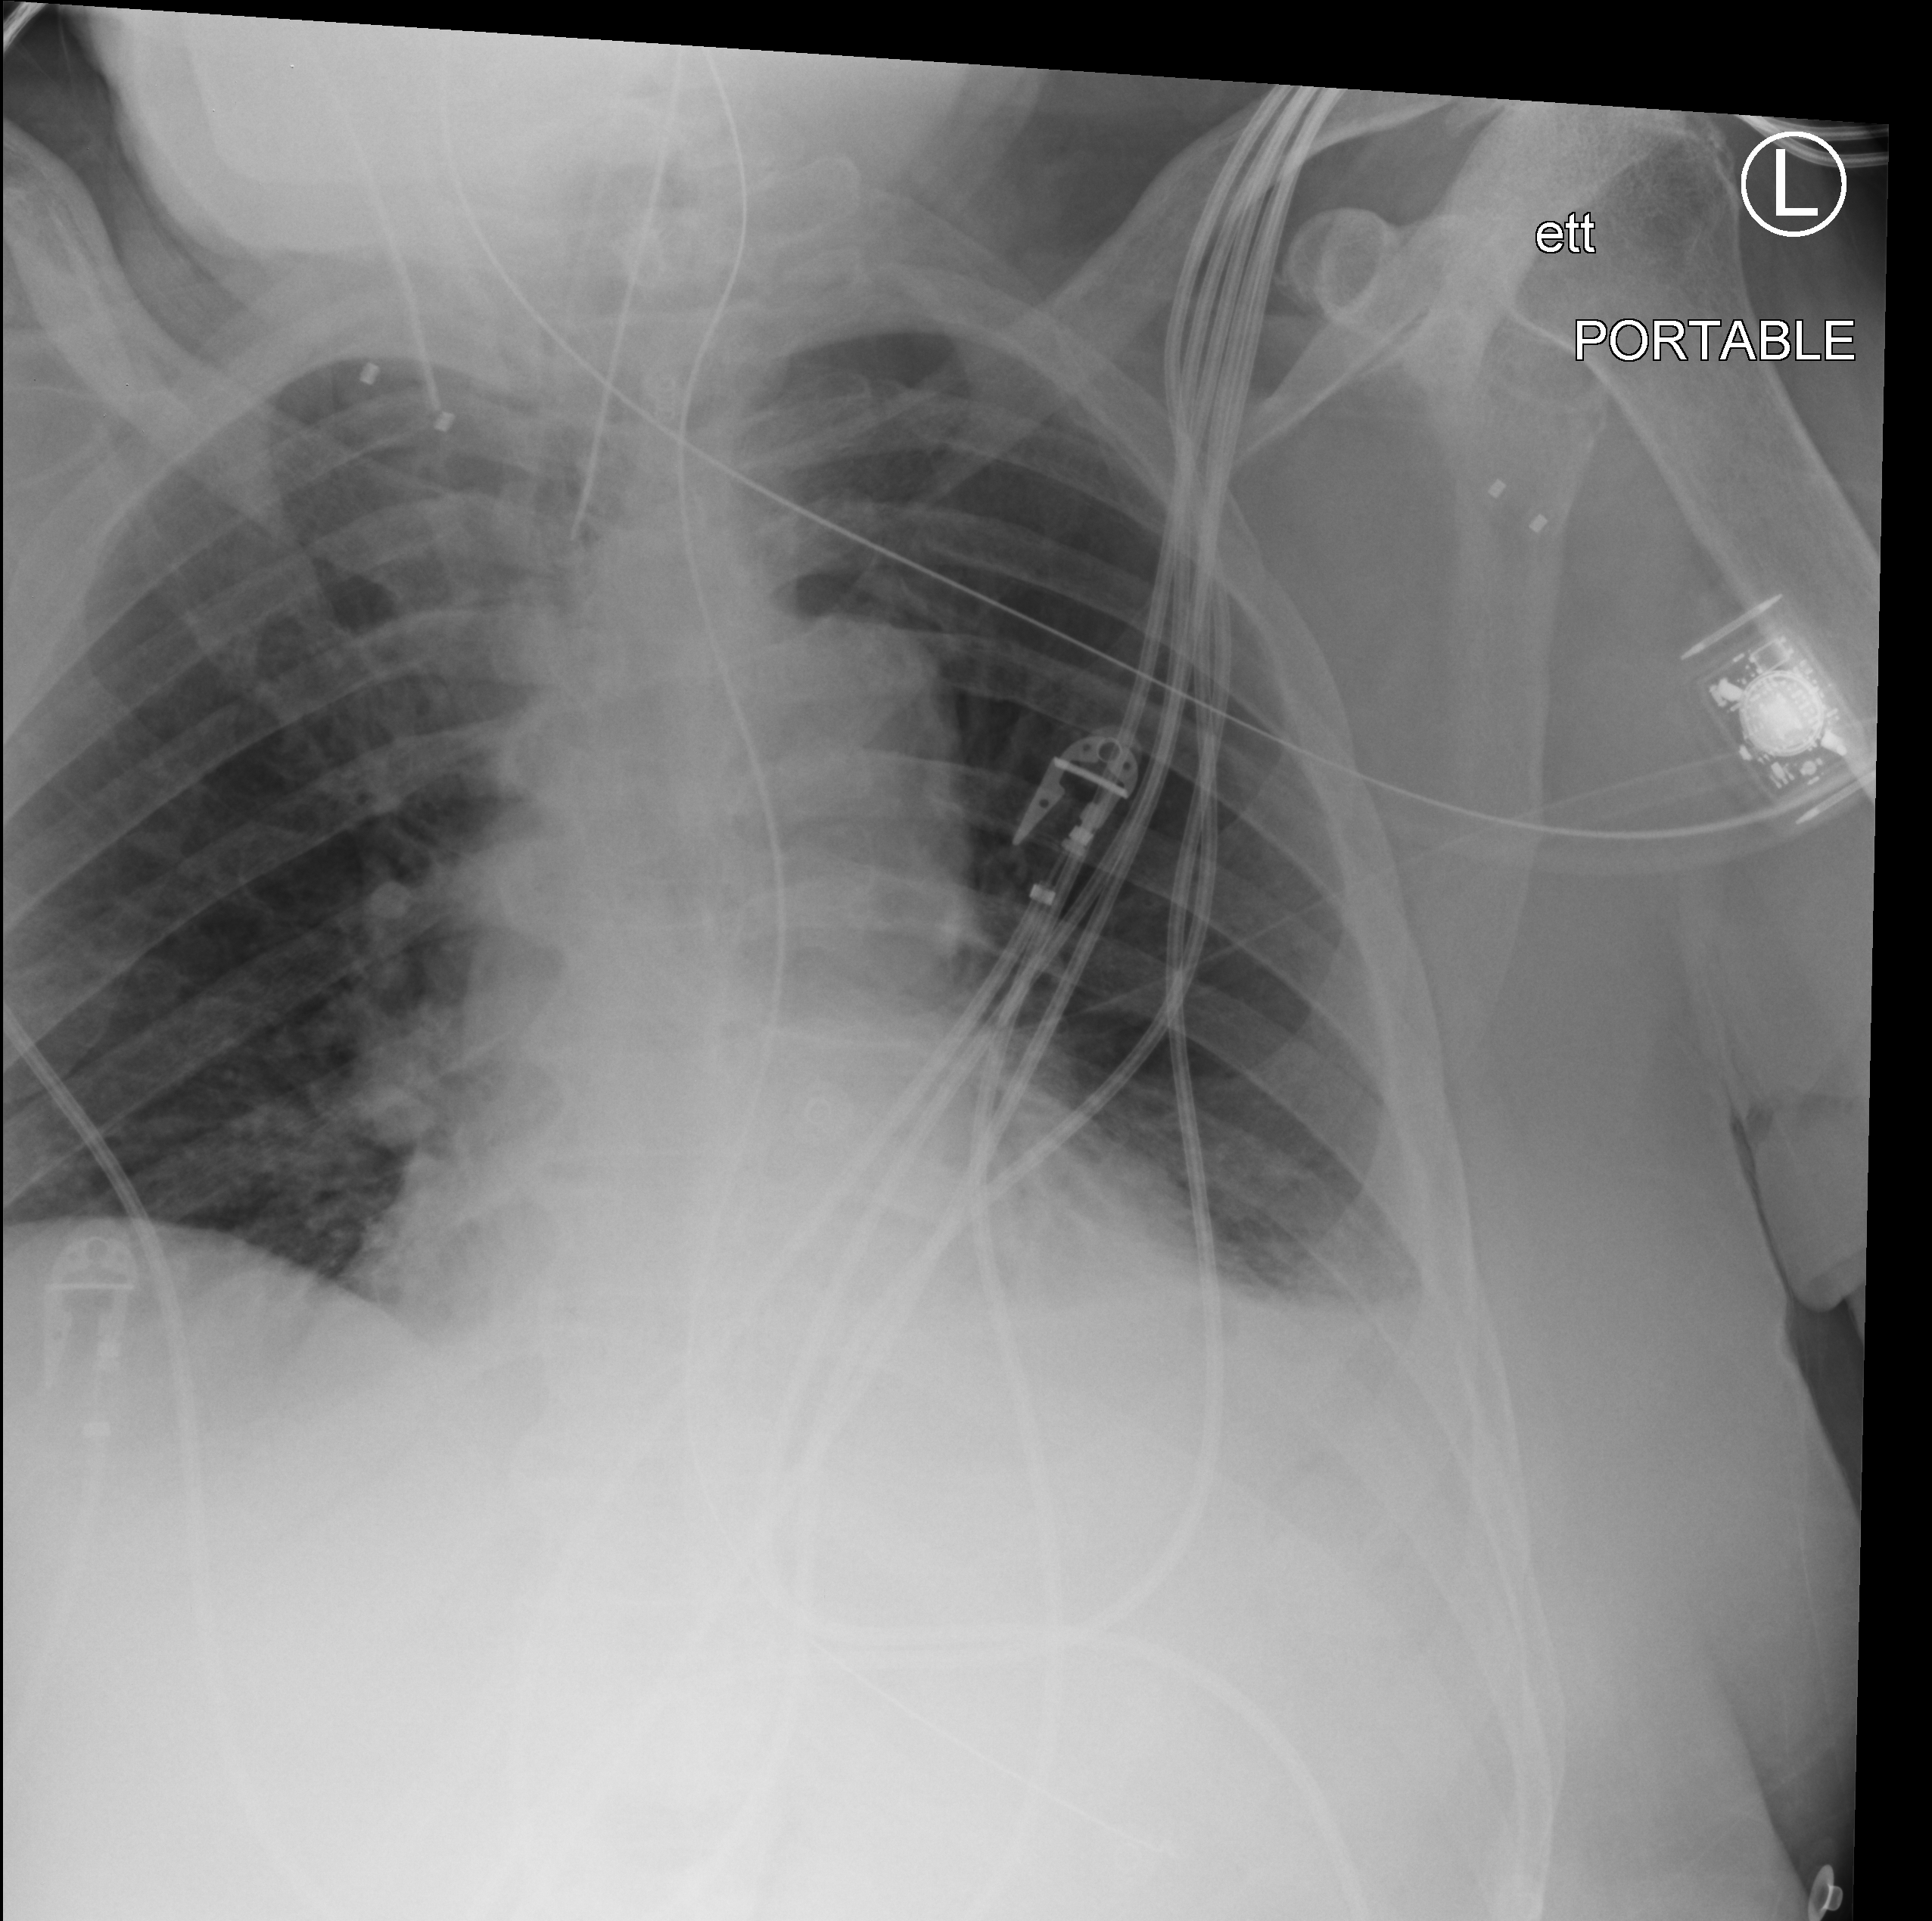
Bedside chest radiograph (computed radiography). Patient hospitalised with COVID-19; male, aged 75–90 years.
From the hospital-stay record, not from the radiograph (when in the stay this image was taken is not recorded): chronic kidney disease (admission record): no.